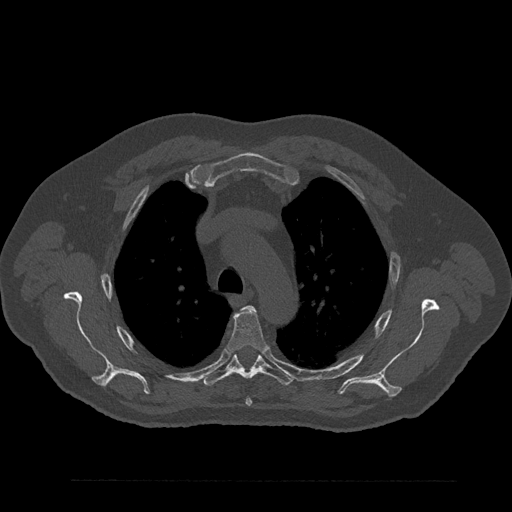
CT including the spine, one axial slice; slice 626 of 797 in the series (ordered by position); 120 kVp; bone window (W 1800 / L 400 HU); 512 × 512 image matrix, field of view 430 × 430 mm. Patient: male, 61 years. From the clinical record (not read from this slice): primary cancer: prostate.
Outlined on this slice (semi-automatically segmented with operator editing):
- T3 vertebra: bounding box [x1, y1, x2, y2] px = [249, 306, 253, 308]
- T4 vertebra: [228, 306, 268, 406]
- T5 vertebra: [203, 354, 292, 386]